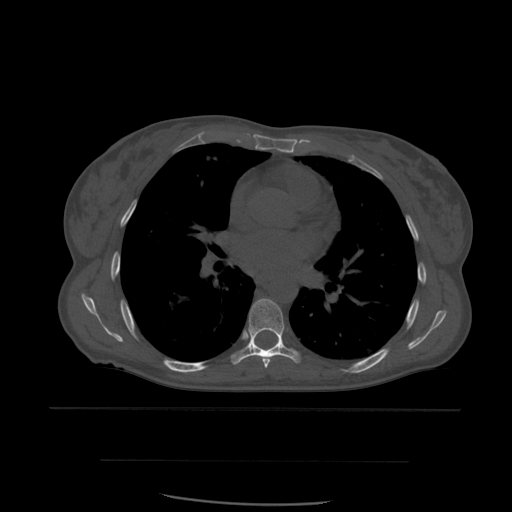
CT including the spine, one axial slice; position 378 of 574 along the scan axis; bone window (W 1800 / L 400 HU); 512 × 512 image matrix, field of view 392 × 392 mm. Patient age 48 years. Case-level facts recorded for this patient, not image findings: primary cancer: lung; vertebrae with lytic lesions (as recorded): T11.
Annotated regions visible in this slice (semi-automatically segmented with operator editing):
- T6 vertebra: bounding box (x1, y1, x2, y2) in pixels: (261, 357, 272, 368)
- T7 vertebra: (231, 299, 300, 365)